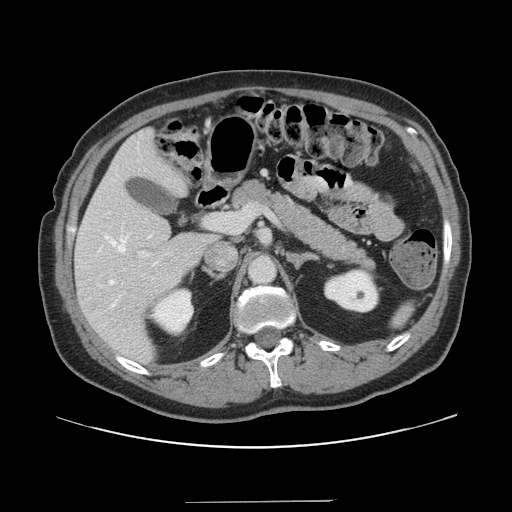
Contrast-enhanced abdominal CT, one axial slice. Position 84 of 151 along the scan axis. Soft-tissue window (W 400 / L 40 HU). 2.5 mm slice thickness. 512 × 512 image matrix. Male patient, age 63 years. From the clinical record (not read from this slice): diagnosis: colorectal cancer liver metastases, imaged before liver resection; multiple liver metastases: no; largest metastasis: 2.1 cm; disease in both lobes: no.
Annotated regions visible in this slice (manually delineated by an expert):
- hepatic veins: bounding box [x1, y1, x2, y2] px = [105, 235, 127, 307]
- liver: [76, 130, 216, 364]
- planned liver remnant (the part of the liver to remain after resection): [76, 130, 215, 364]
- portal vein (with intrahepatic branches): [138, 206, 254, 257]